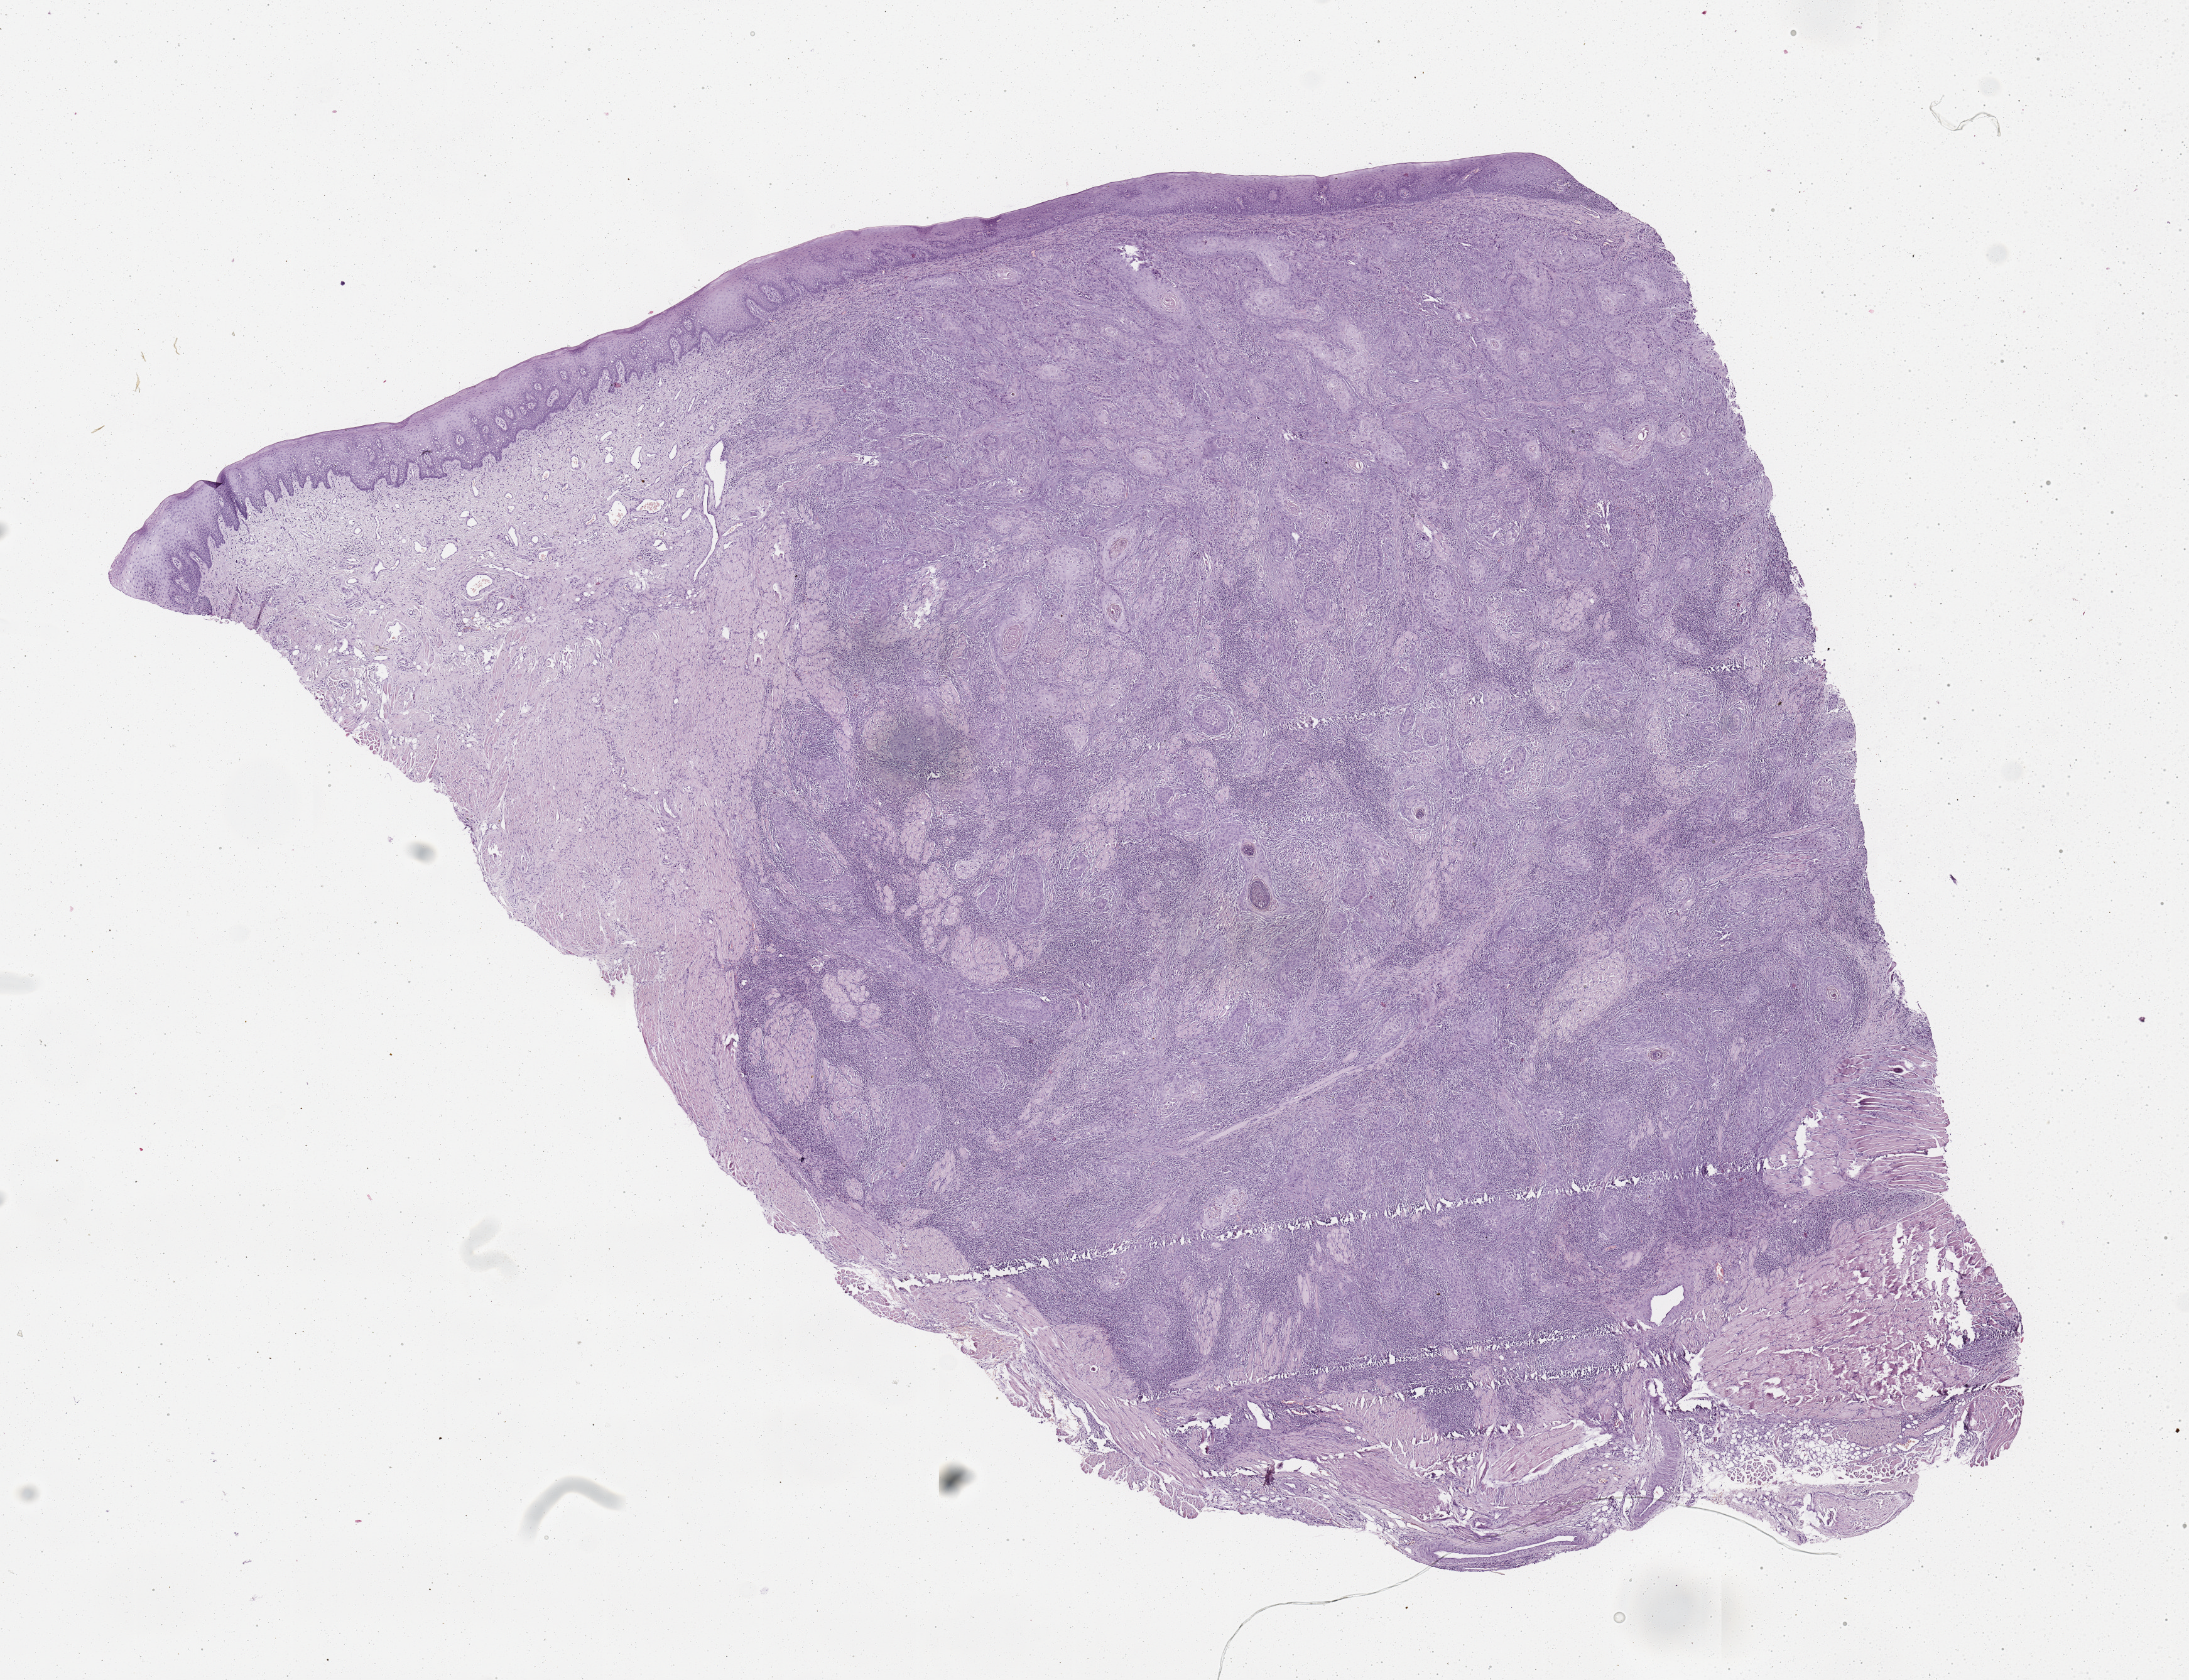
Hematoxylin and eosin (H&E) stained whole-slide image, shown as a low-resolution overview of the whole scanned area (about 13.8 x 10.6 mm, from a 20x scan), tumour tissue sample, sampled site: tongue. Patient: male, age 61 years. Composition of this section per pathologist review: tumour nuclei 80%, necrosis 0%.
Histologic diagnosis: Squamous cell carcinoma, NOS (tongue, NOS).